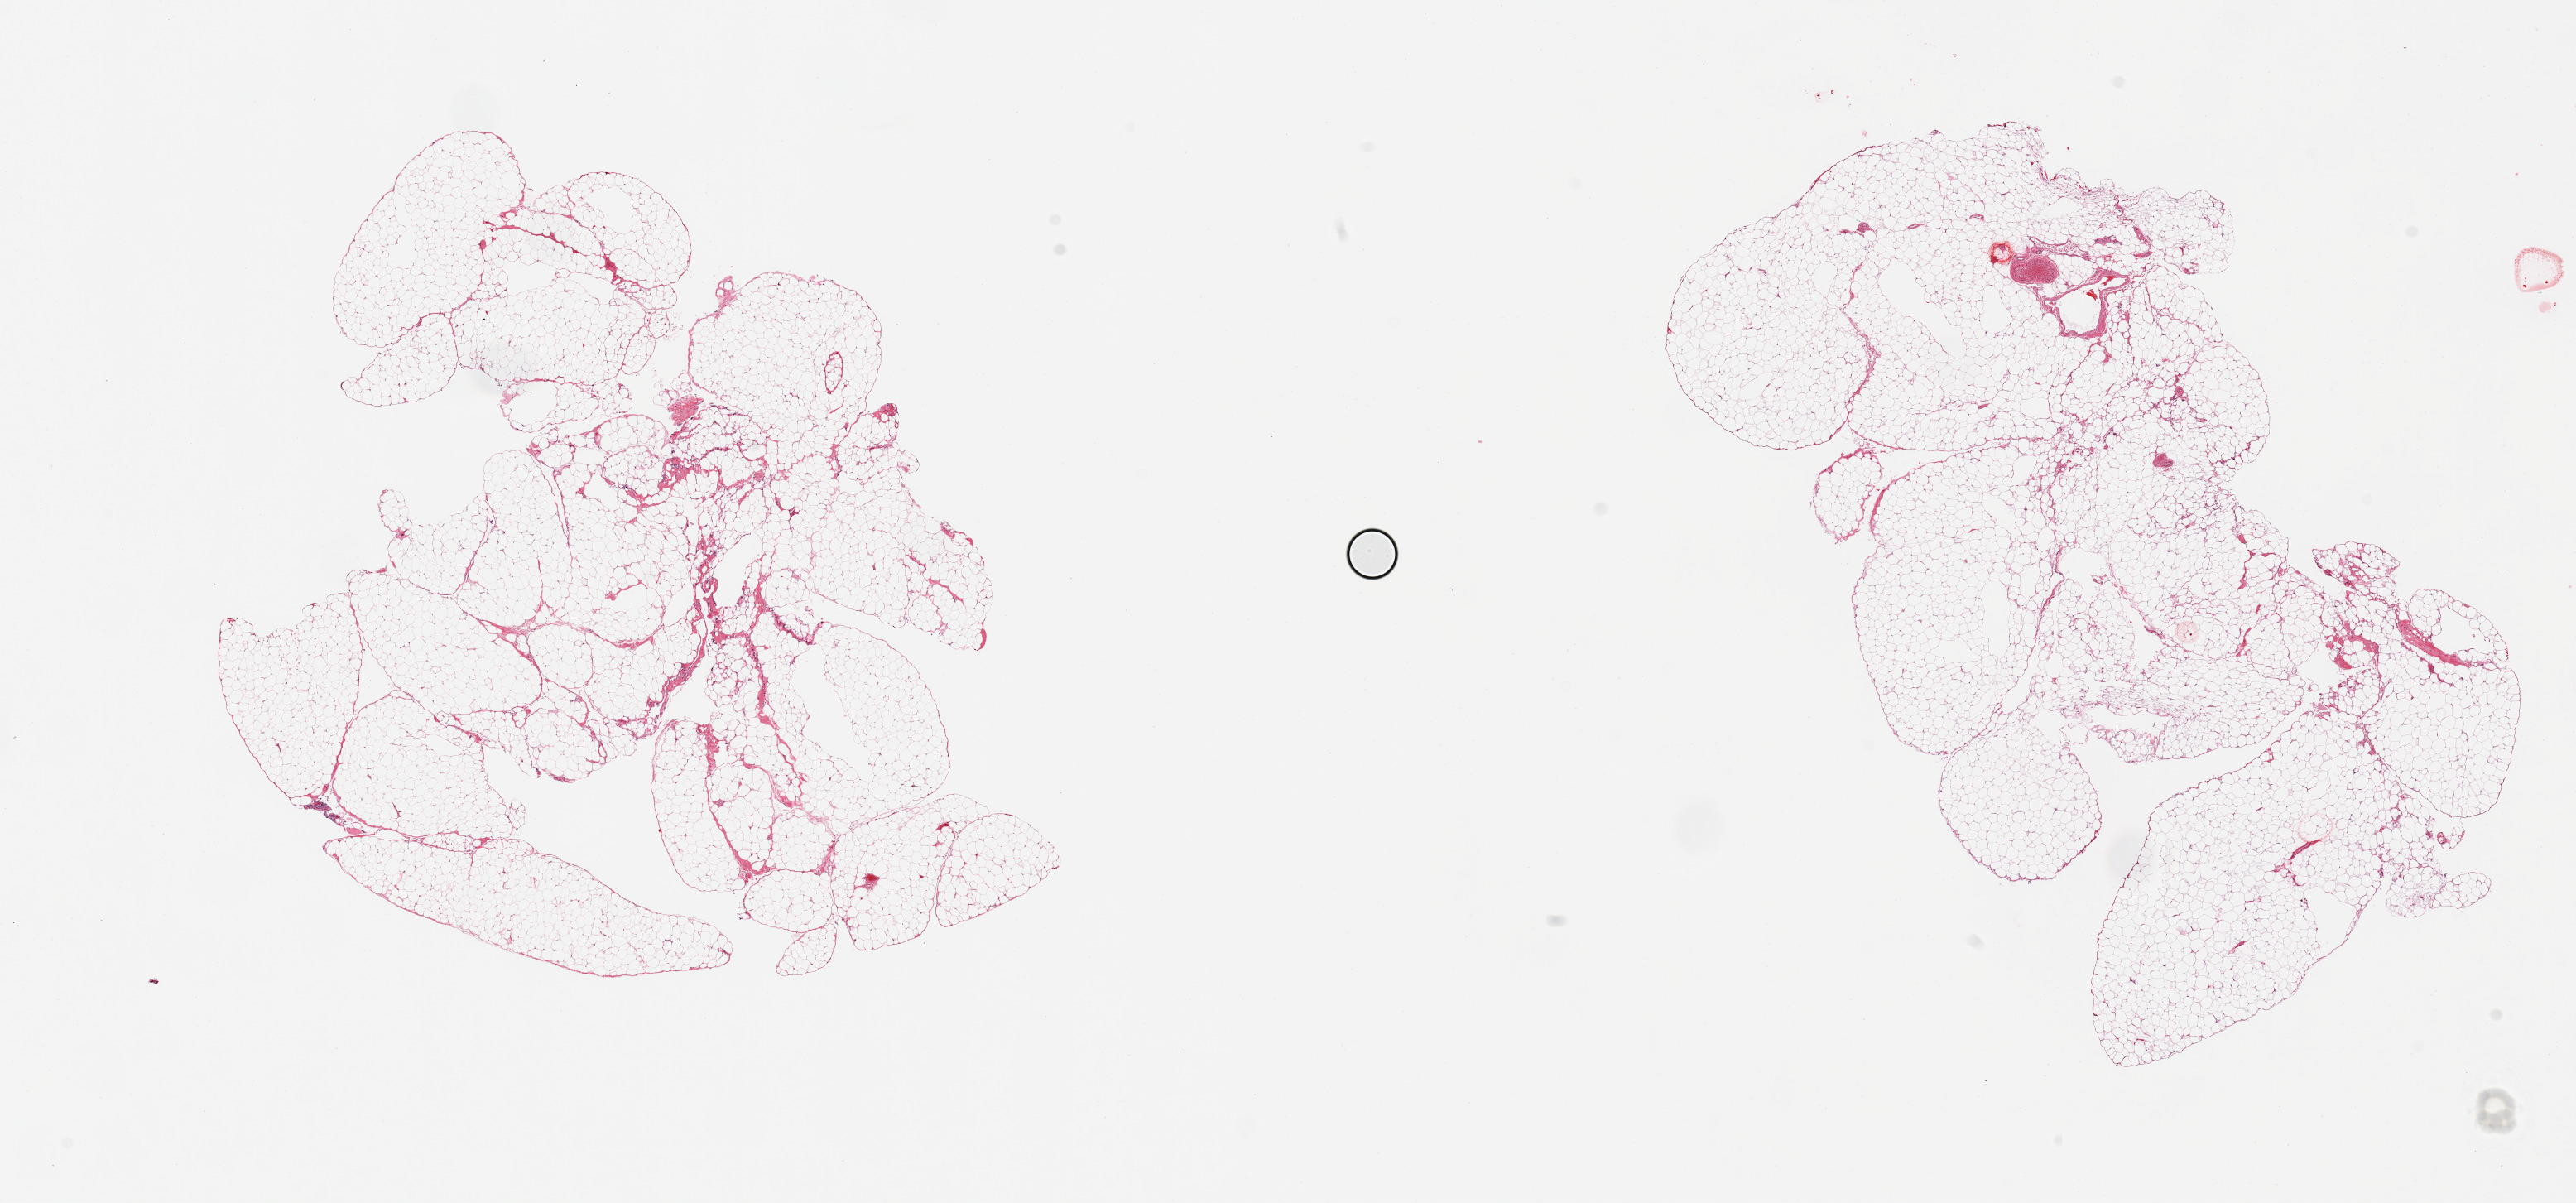
Whole-slide image, haematoxylin and eosin stain, low-resolution overview of the scanned area, about 24.6 x 11.5 mm, PAXgene-fixed, paraffin-embedded tissue, section of omentum (target tissue), tissue donor sample. Male donor.
* pathologist's review note for this sample: 2 pieces